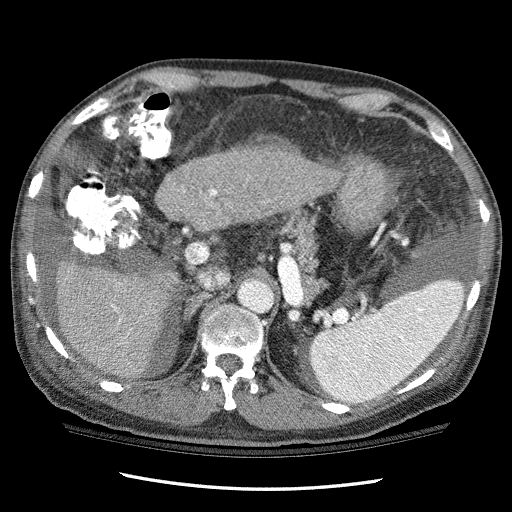
Contrast-enhanced abdominal CT (liver protocol), one axial slice; slice 65 of 114 in the series (ordered by position); 120 kVp; one of 3 acquisitions stored at this slice position; soft-tissue window (W 400 / L 40 HU); 2.5 mm slice thickness; 512 × 512 image matrix, field of view 360 × 360 mm. Case-level facts recorded for this patient, not image findings: diagnosis: hepatocellular carcinoma (patient treated with transarterial chemoembolisation; whether this scan precedes or follows treatment is not stated here); TNM stage (as recorded): Stage-I; Child-Pugh class: C; tumour differentiation: well differentiated; tumour nodularity: uninodular.
Annotated regions visible in this slice (semi-automatic segmentation, software-assisted and operator-edited):
- liver parenchyma outside the tumour (the mass and vessels are separate outlines, so this box may not span the whole liver): bounding box (x1, y1, x2, y2) in pixels: (56, 142, 342, 380)
- mass: (244, 133, 301, 199)
- liver vessels: (112, 189, 217, 324)